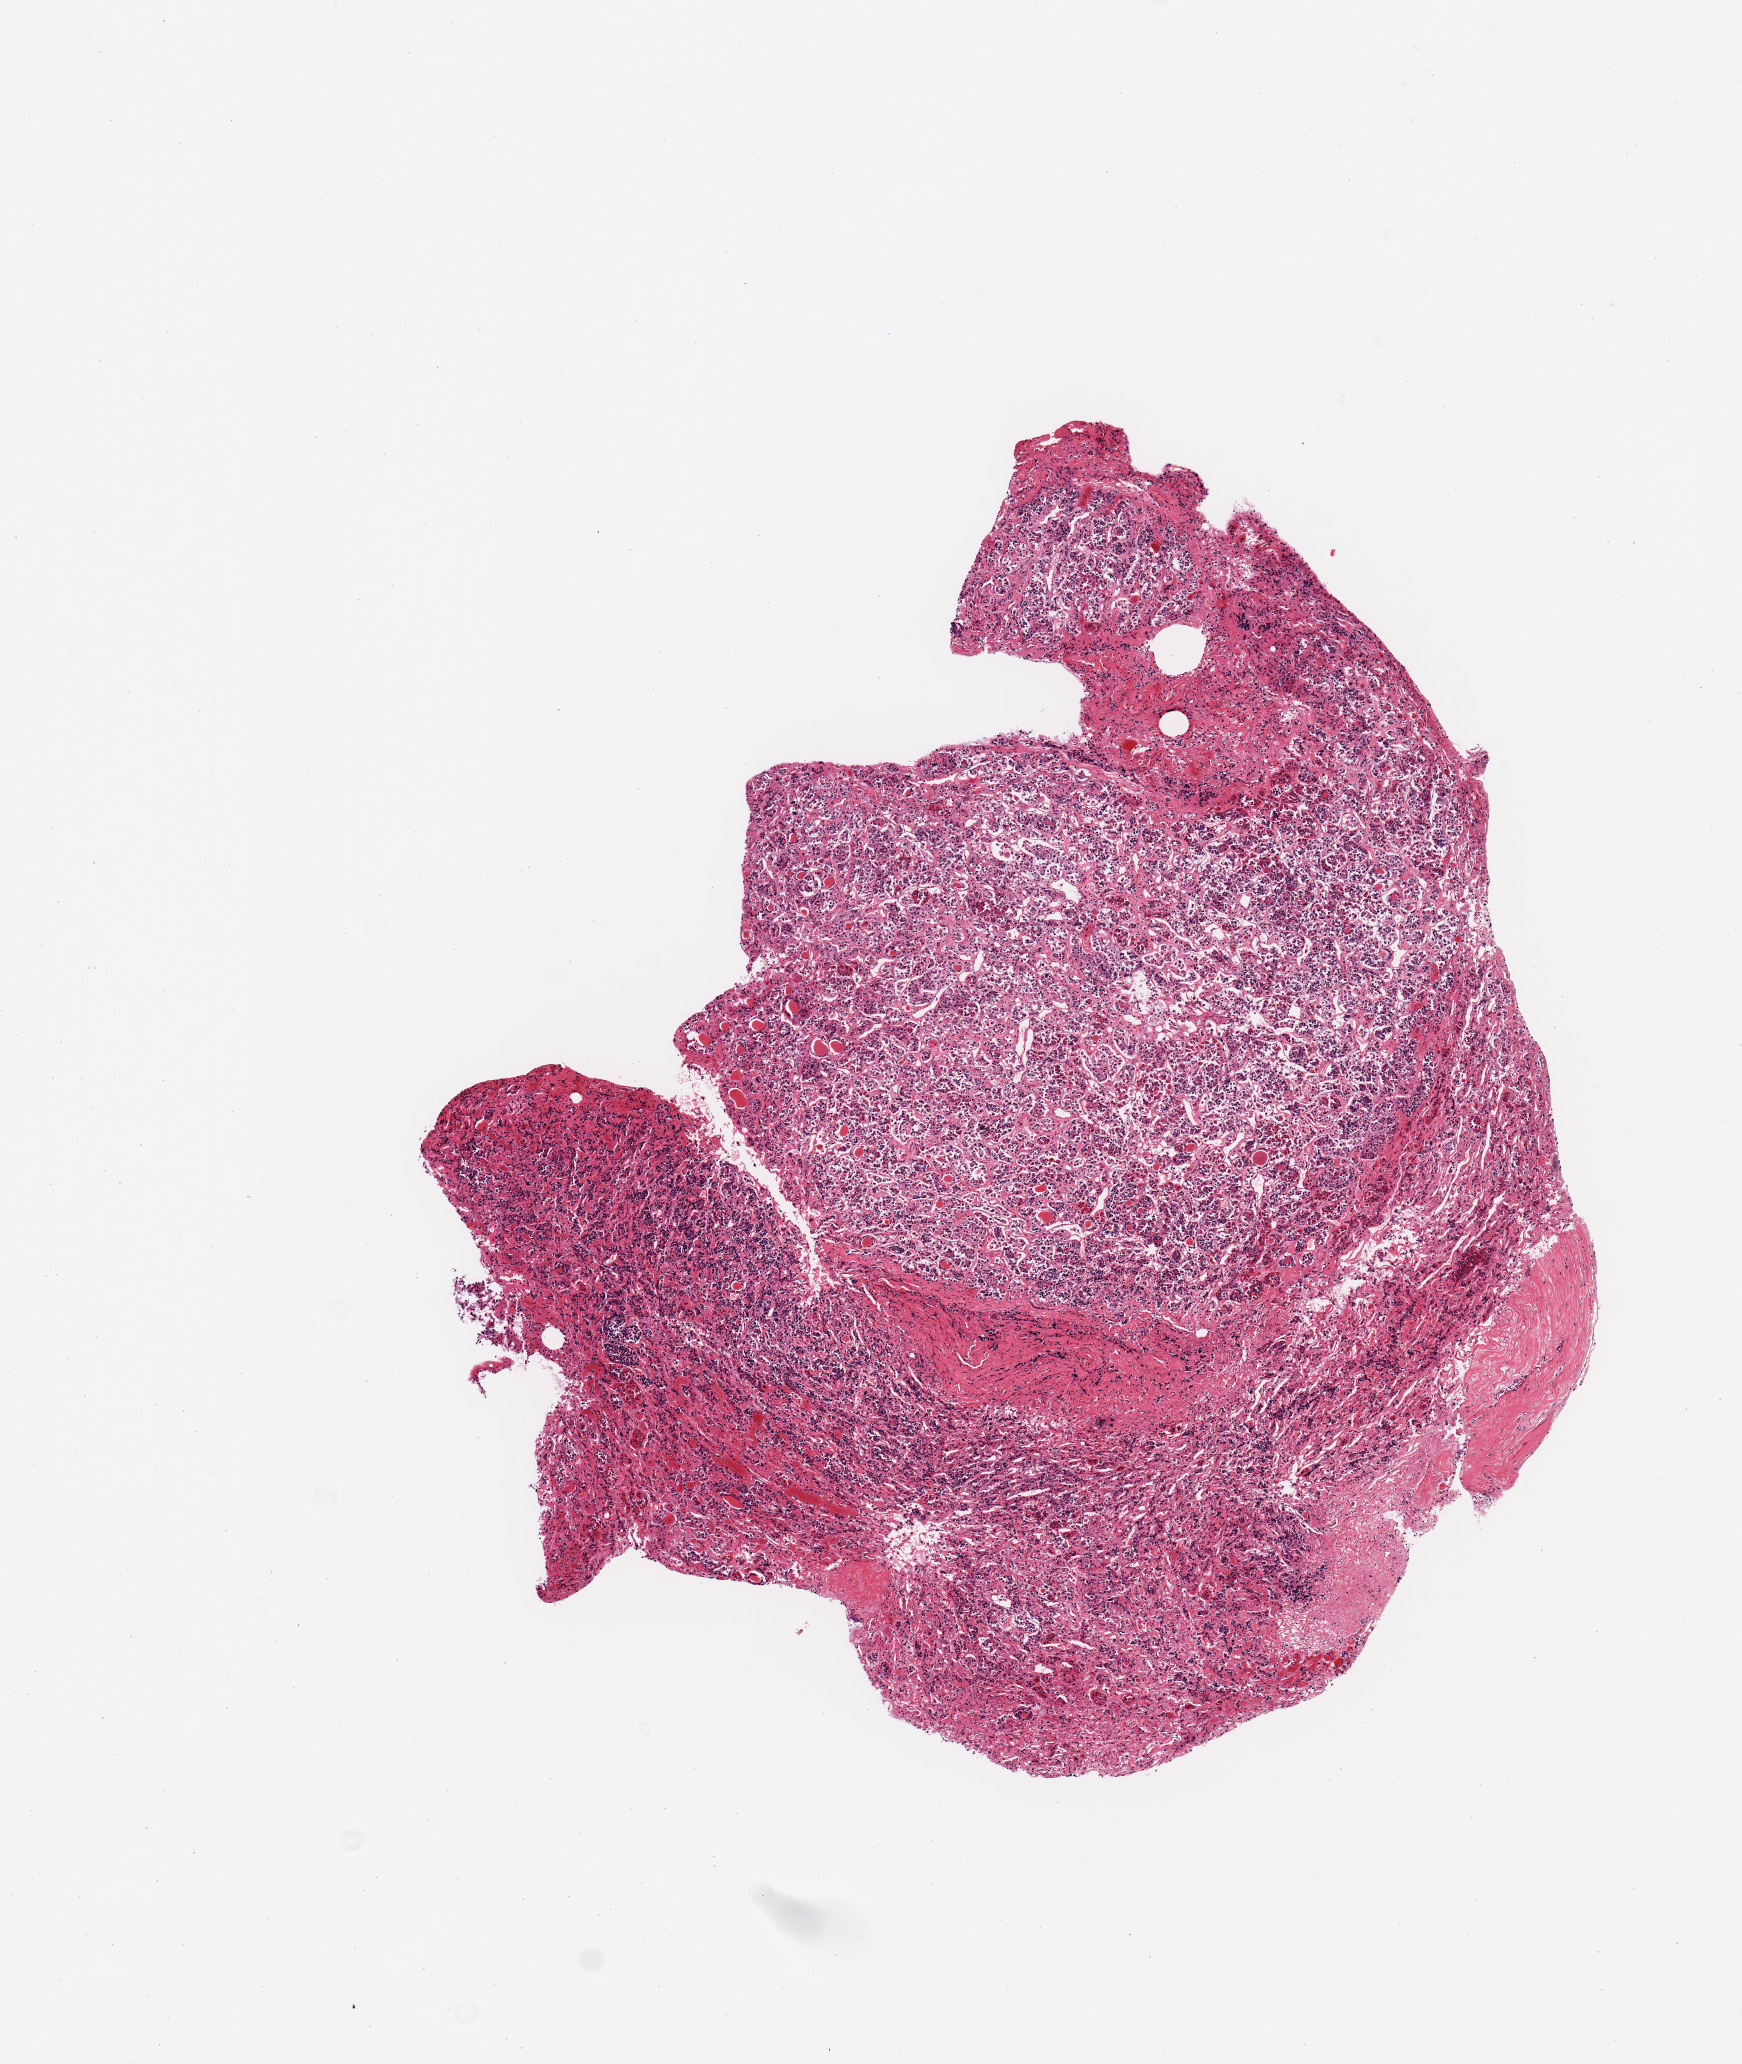
Whole-slide image, hematoxylin and eosin (H&E) stain, low-resolution overview of the scanned area, about 6.9 x 8.2 mm, PAXgene-fixed, paraffin-embedded tissue, sampled site (target tissue): pituitary, tissue donor sample. Donor sex: male.
Review note (as recorded): 1 piece, adenohypophysis.